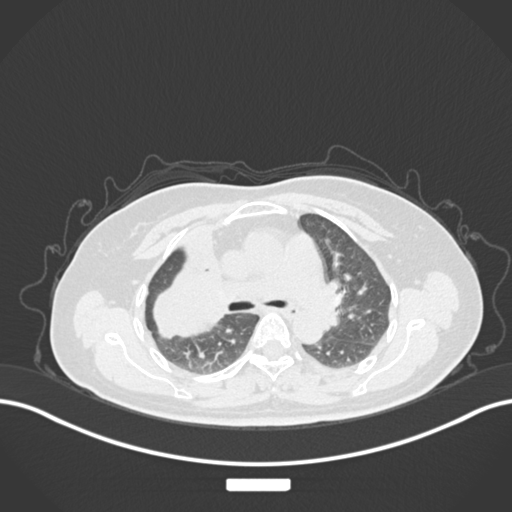
Chest CT, one axial slice. Position 98 of 177 along the scan axis. 120 kVp. Lung window (W 1500 / L -600 HU). 1 mm slice thickness. 512 × 512 image matrix. Female patient, age 60 years. Case-level facts recorded for this patient, not image findings: clinical TNM (as recorded): T3 N1 M1.
Structures marked on this image (rectangle marked by the reading radiologist):
- lung tumour (recorded histology: adenocarcinoma): bounding box (x1, y1, x2, y2) in pixels: (144, 253, 229, 341)